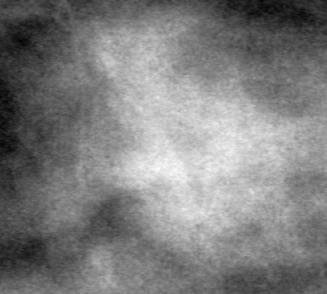
Crop from a digitized film mammogram around one marked abnormality, left breast, CC view, BI-RADS breast density category 3 (scale 1–4).
- Finding: mass, shape oval, margins obscured; BI-RADS assessment category 4; pathology (as recorded): benign.